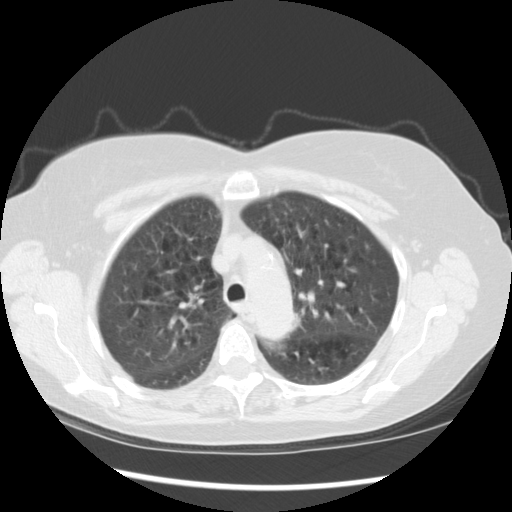
Chest CT (low-dose screening protocol), one axial image; baseline annual screen; lung window (W 1500 / L -600 HU); 2.5 mm slice thickness; slice 96 of 123 in the series; 512 × 512 image matrix, field of view 360 × 360 mm. Female participant, aged 70 years at enrolment. Current smoker at enrolment.
Lesion marked by an expert reader, box from (x=276, y=296) to (x=324, y=352) px. No non-calcified nodule or mass ≥4 mm was recorded by the screening reader at this exam. Later outcome: lung cancer diagnosed 757 days after this screen — neoplasm, malignant, left upper lobe, stage IIIB (AJCC 6th edition), 40 mm at pathology.